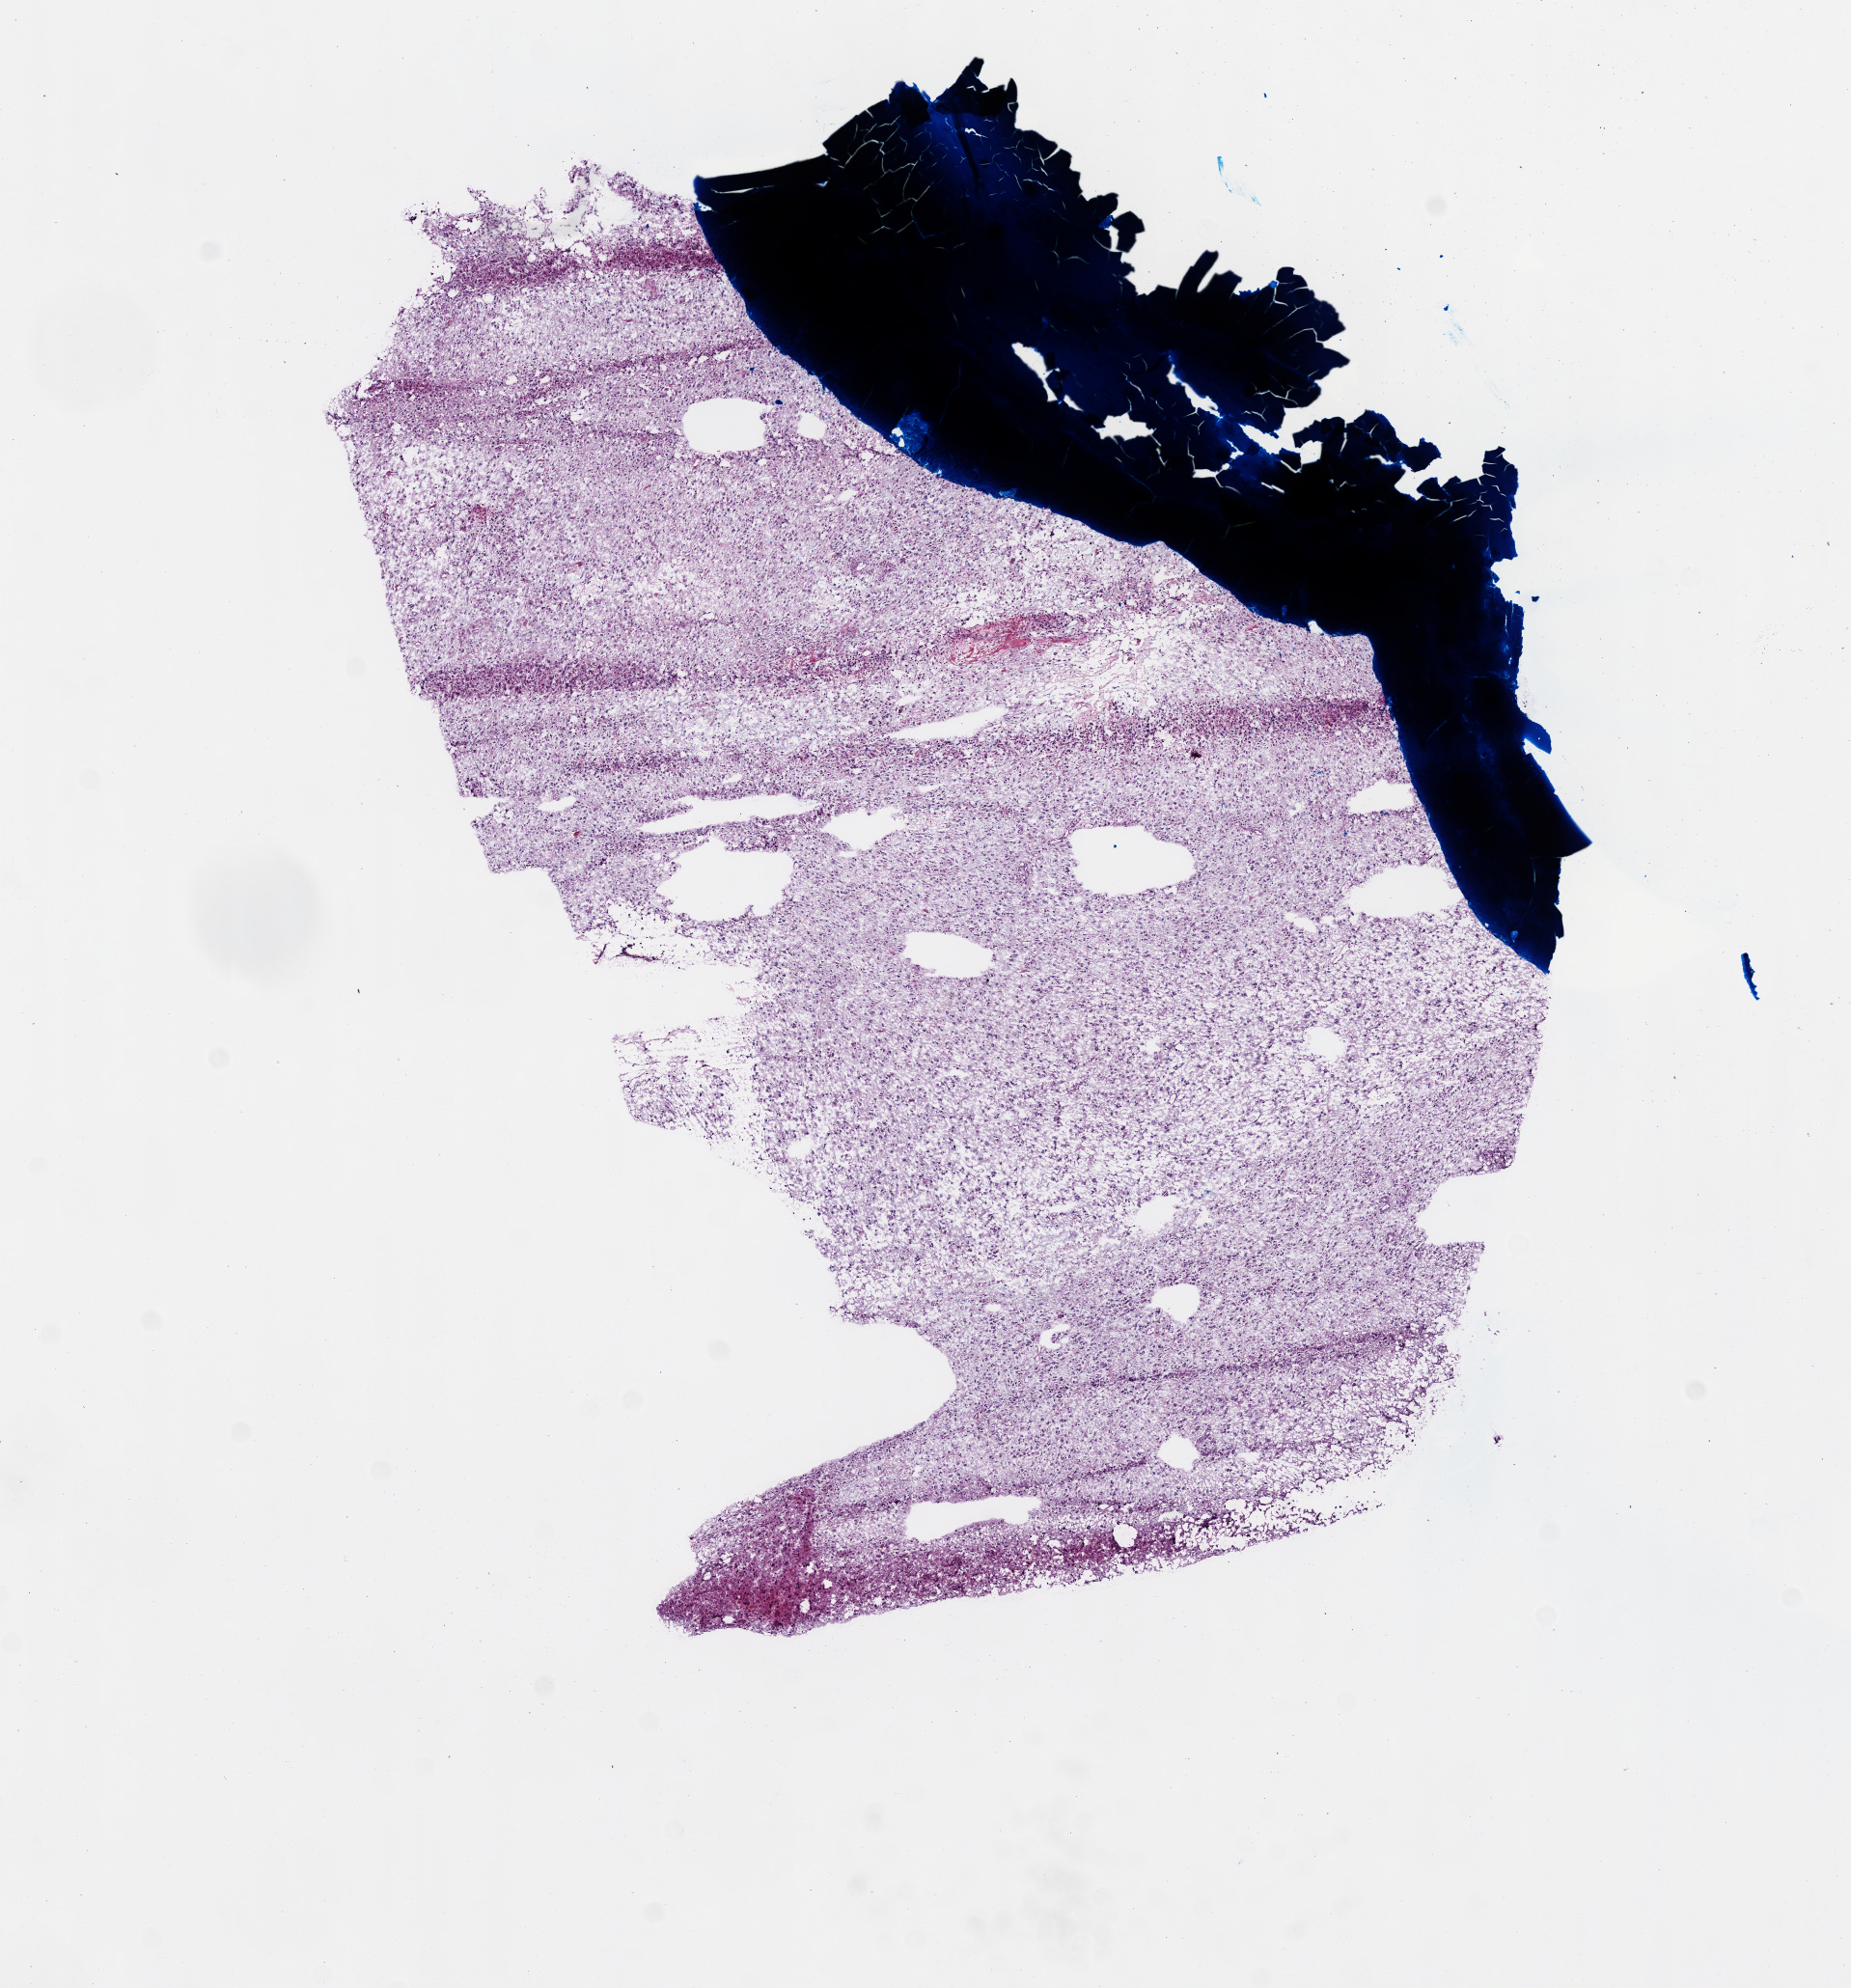
H&E whole-slide image, low-resolution overview of the scanned area, about 7.7 x 8.3 mm, frozen section from the top of the tissue portion, brain, primary tumour sample. Male, age 63 years at initial diagnosis. Slide review estimates, as recorded: tumour cells 80%, tumour nuclei 85%, normal cells 0%, stromal cells 10%, necrosis 10%.
Histologic diagnosis: Glioblastoma.